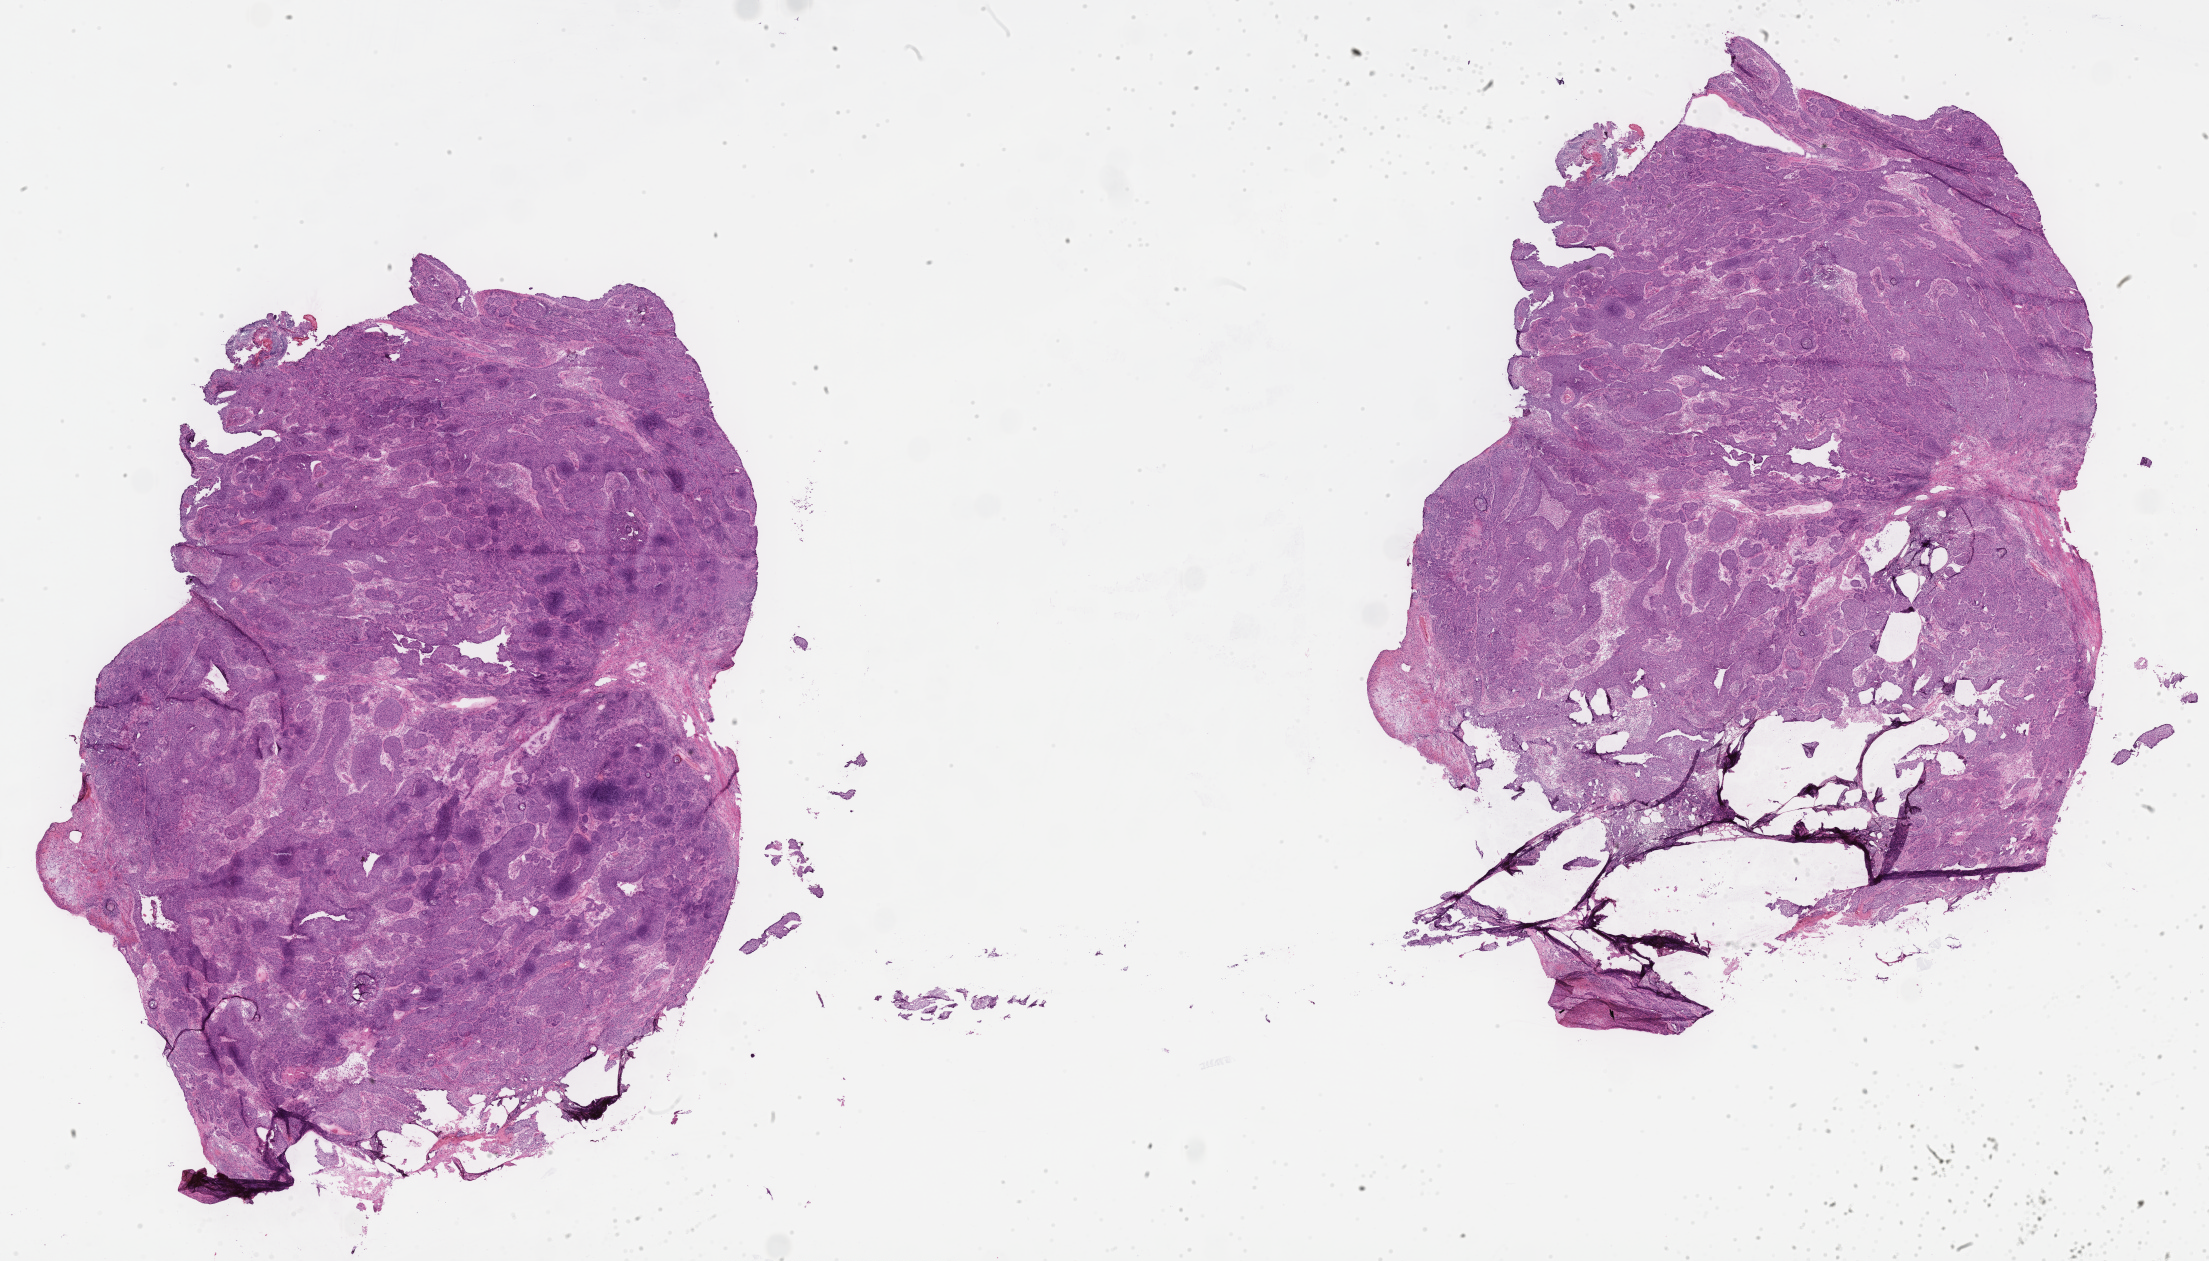
Hematoxylin and eosin (H&E) whole-slide image — low-resolution overview of the scanned area, about 35.7 x 20.4 mm, frozen section, primary tumor, anatomic site: breast (left). Female, age 86 years at initial diagnosis. Pathologist review of this section (percent, as recorded): tumor cells 80%, tumor nuclei 80%, stromal cells 20%, necrosis 0%, normal cells 0%. Infiltration values recorded for this section: lymphocyte infiltration 6%, monocyte infiltration 2%, neutrophil infiltration 8%.
* section: top of the tissue portion
* histologic diagnosis: Infiltrating duct carcinoma, NOS